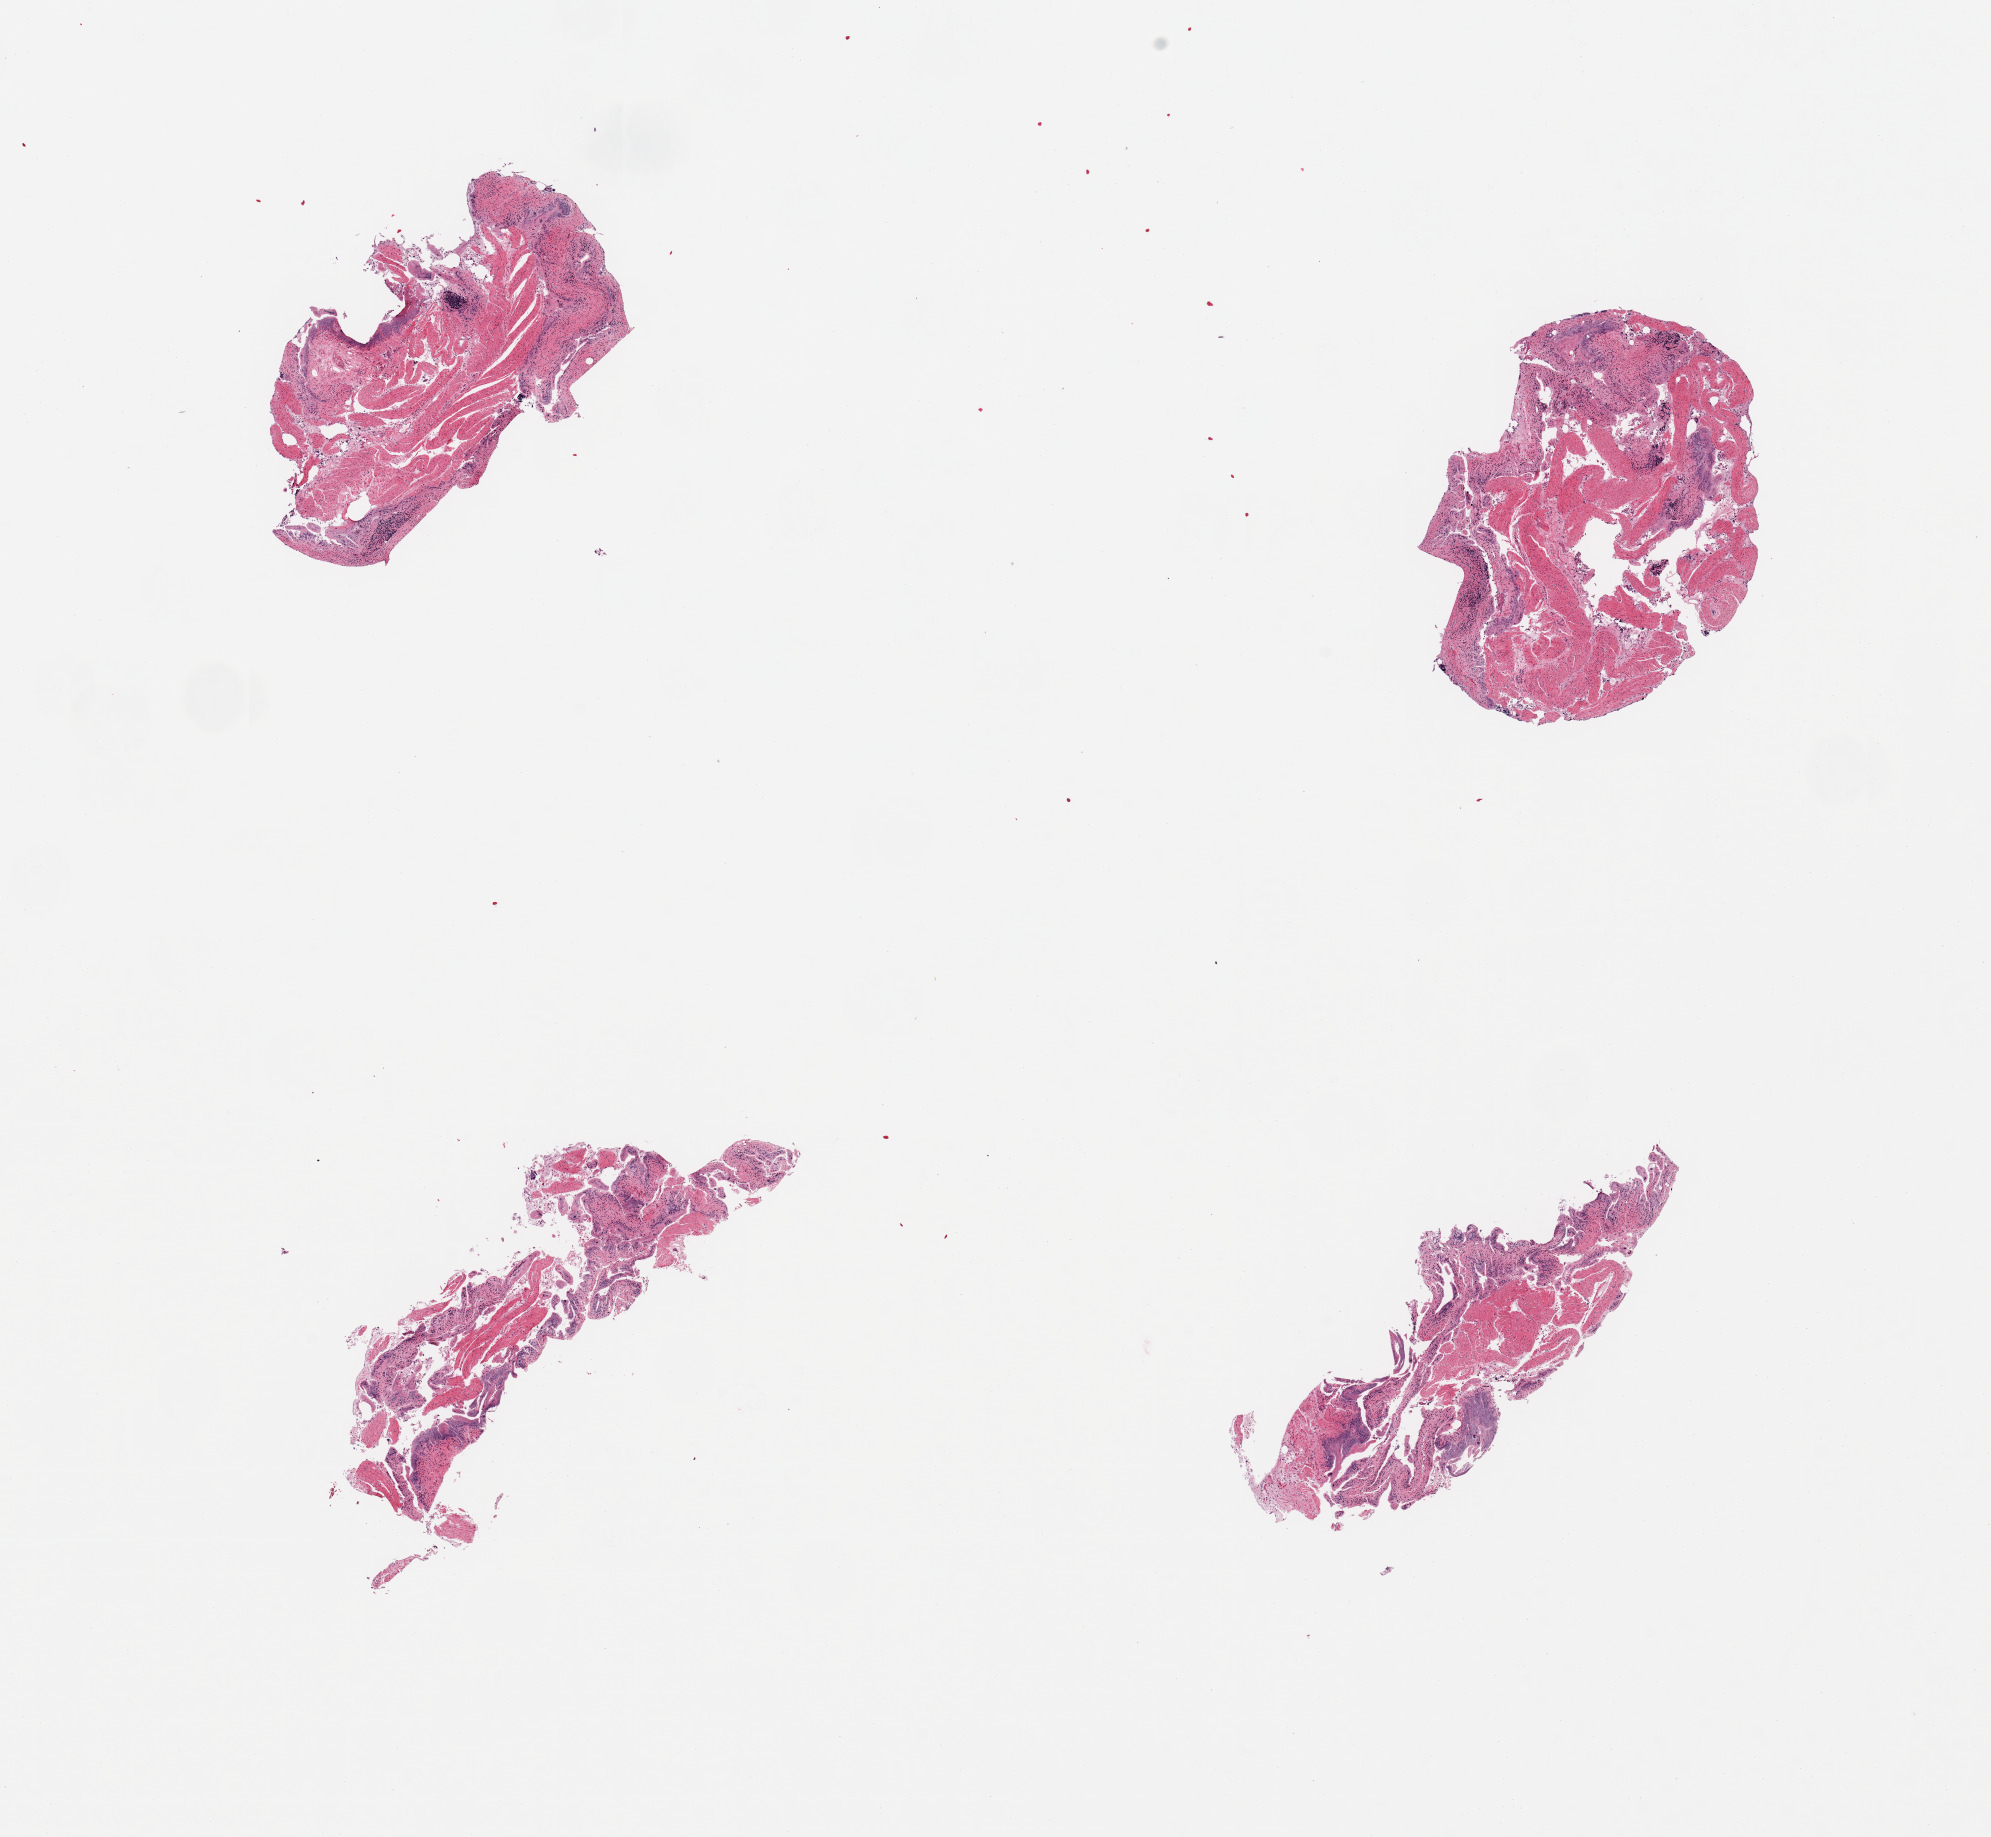
Whole-slide image, H&E stain — low-resolution overview of the scanned area, about 15.8 x 14.5 mm (slide scanned at 20x), PAXgene-fixed paraffin-embedded (PFPE) section, sampled site (target tissue): ileum, tissue donor sample. Donor: male.
* pathologist's review note for this sample: 4 pieces, insufficient target lymphoid aggregates, correct target